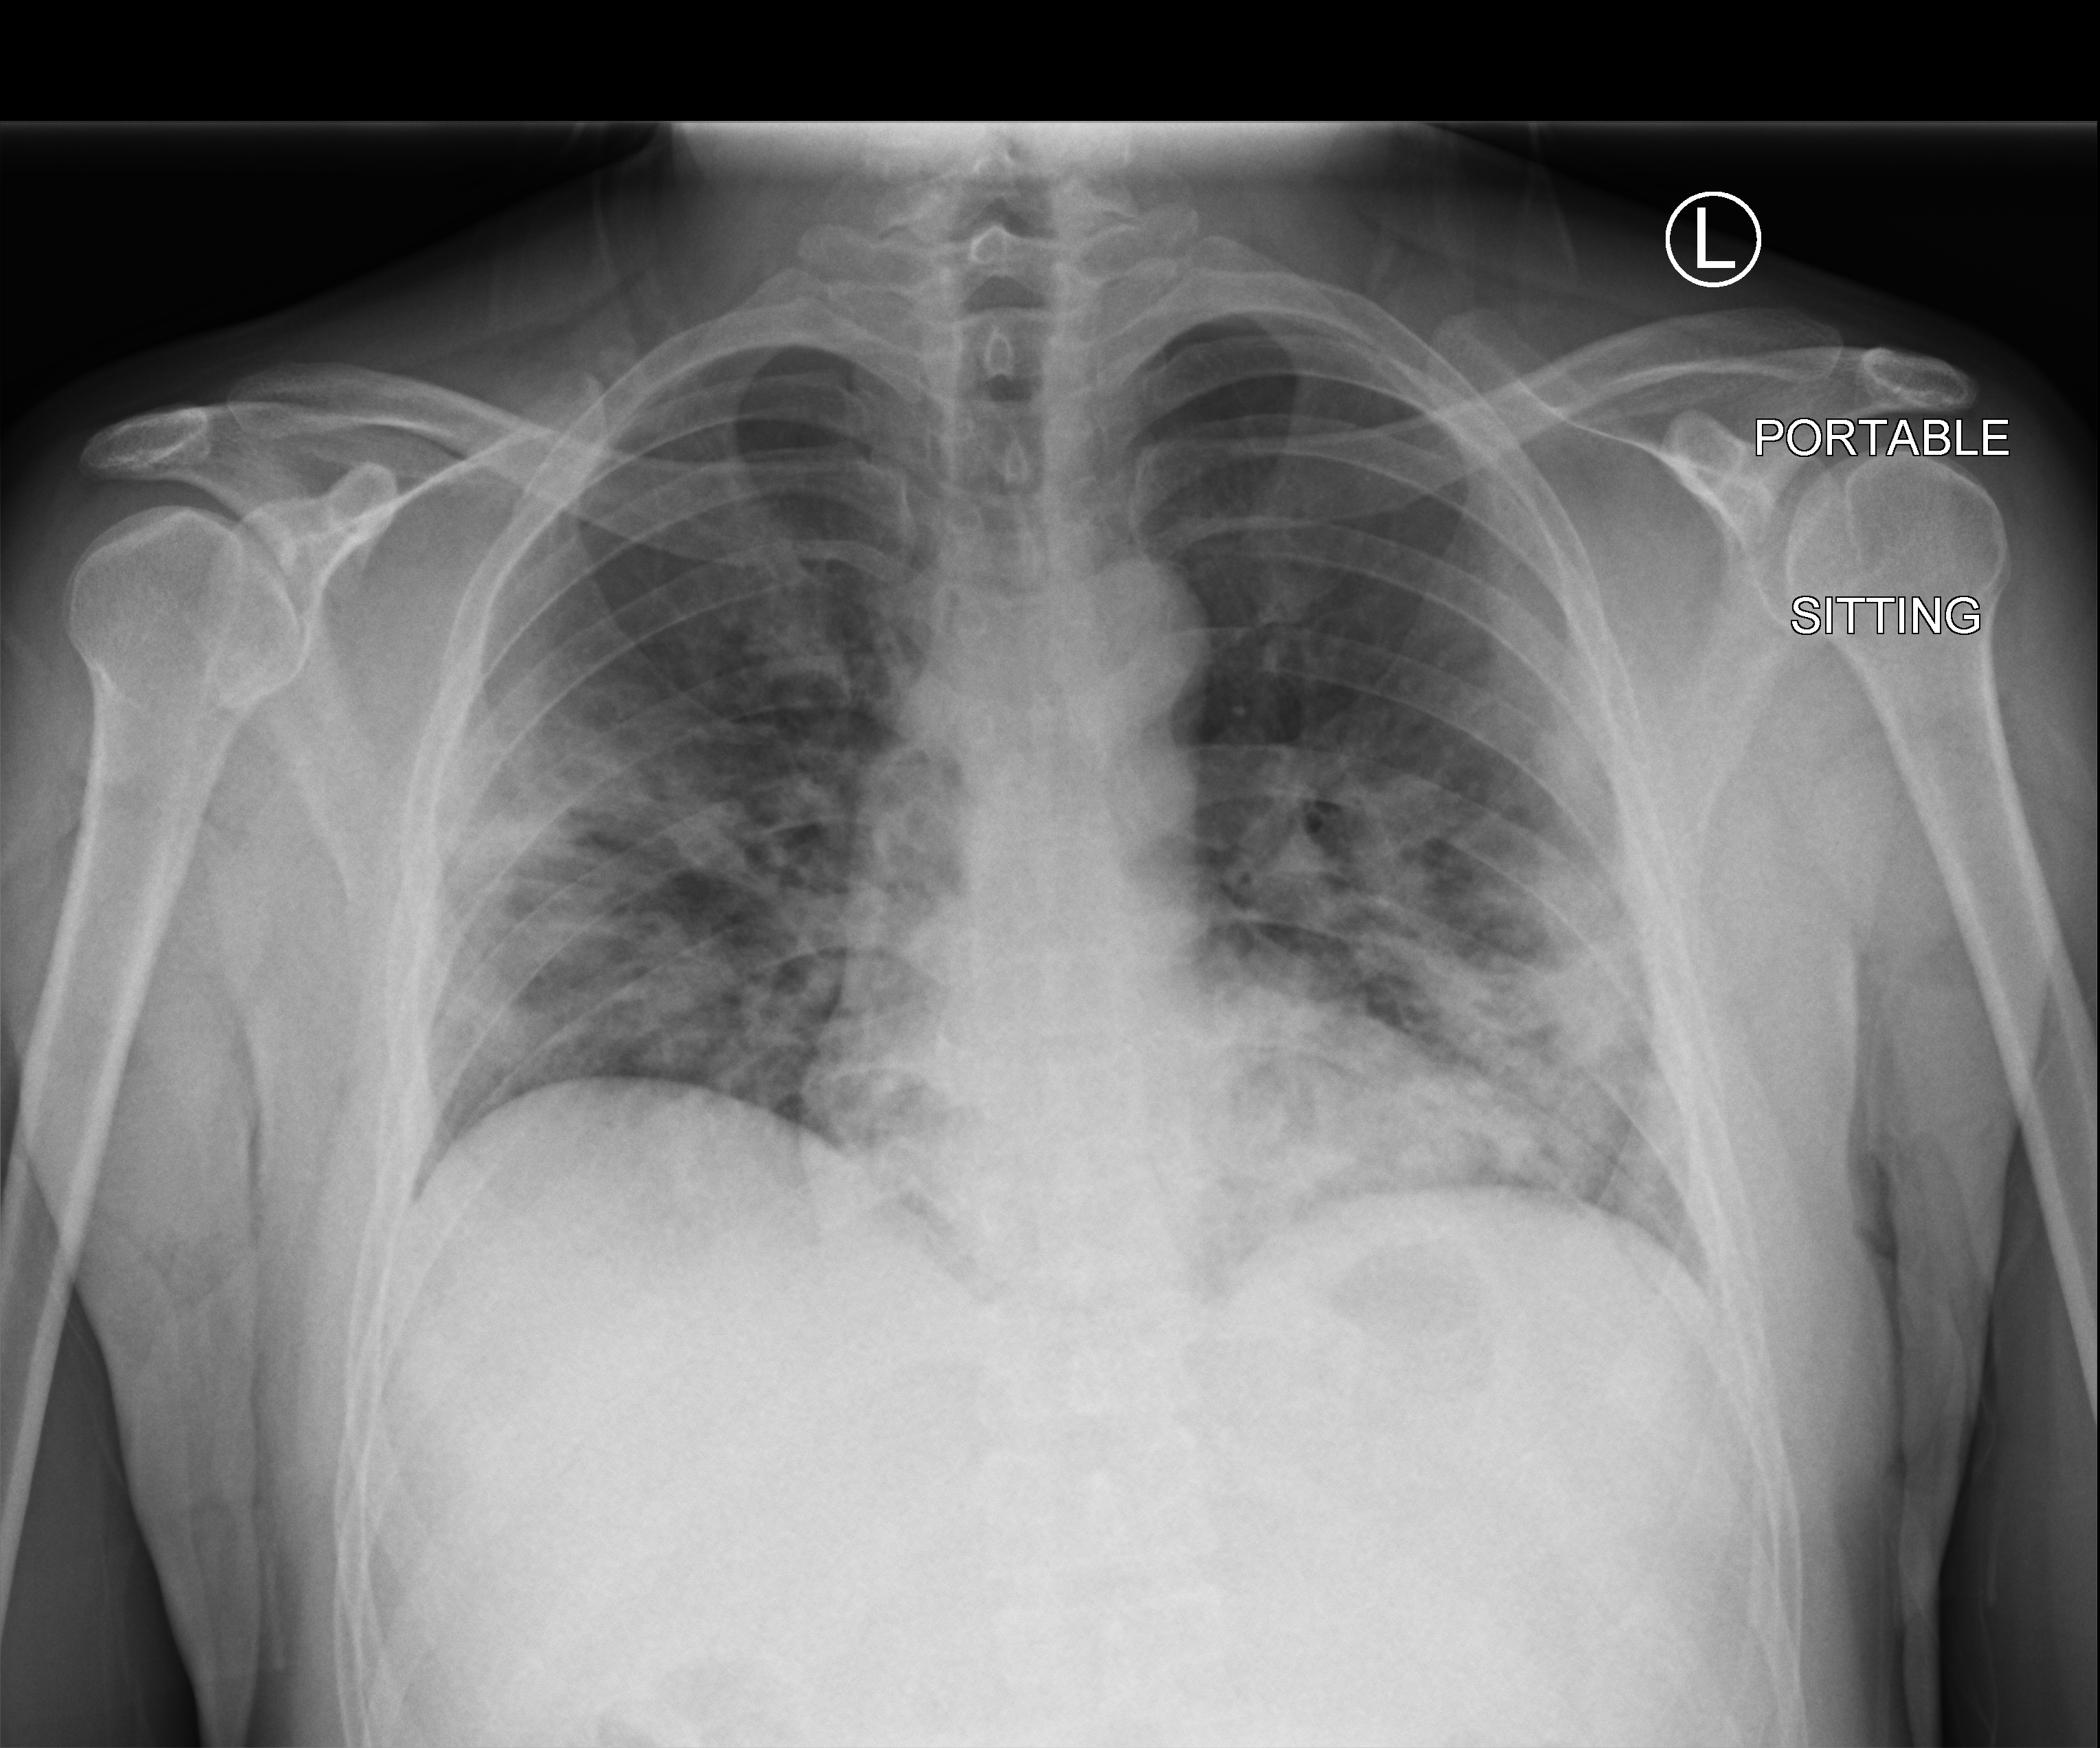
Bedside chest radiograph (computed radiography); anteroposterior (AP) projection. Male patient hospitalised with COVID-19, age 18–59 years.
Admission-level facts for this patient (not findings on this image; timing relative to this image not recorded): admitted to intensive care during this hospital stay: no; mechanically ventilated during this hospital stay: no; chronic kidney disease (admission record): no.